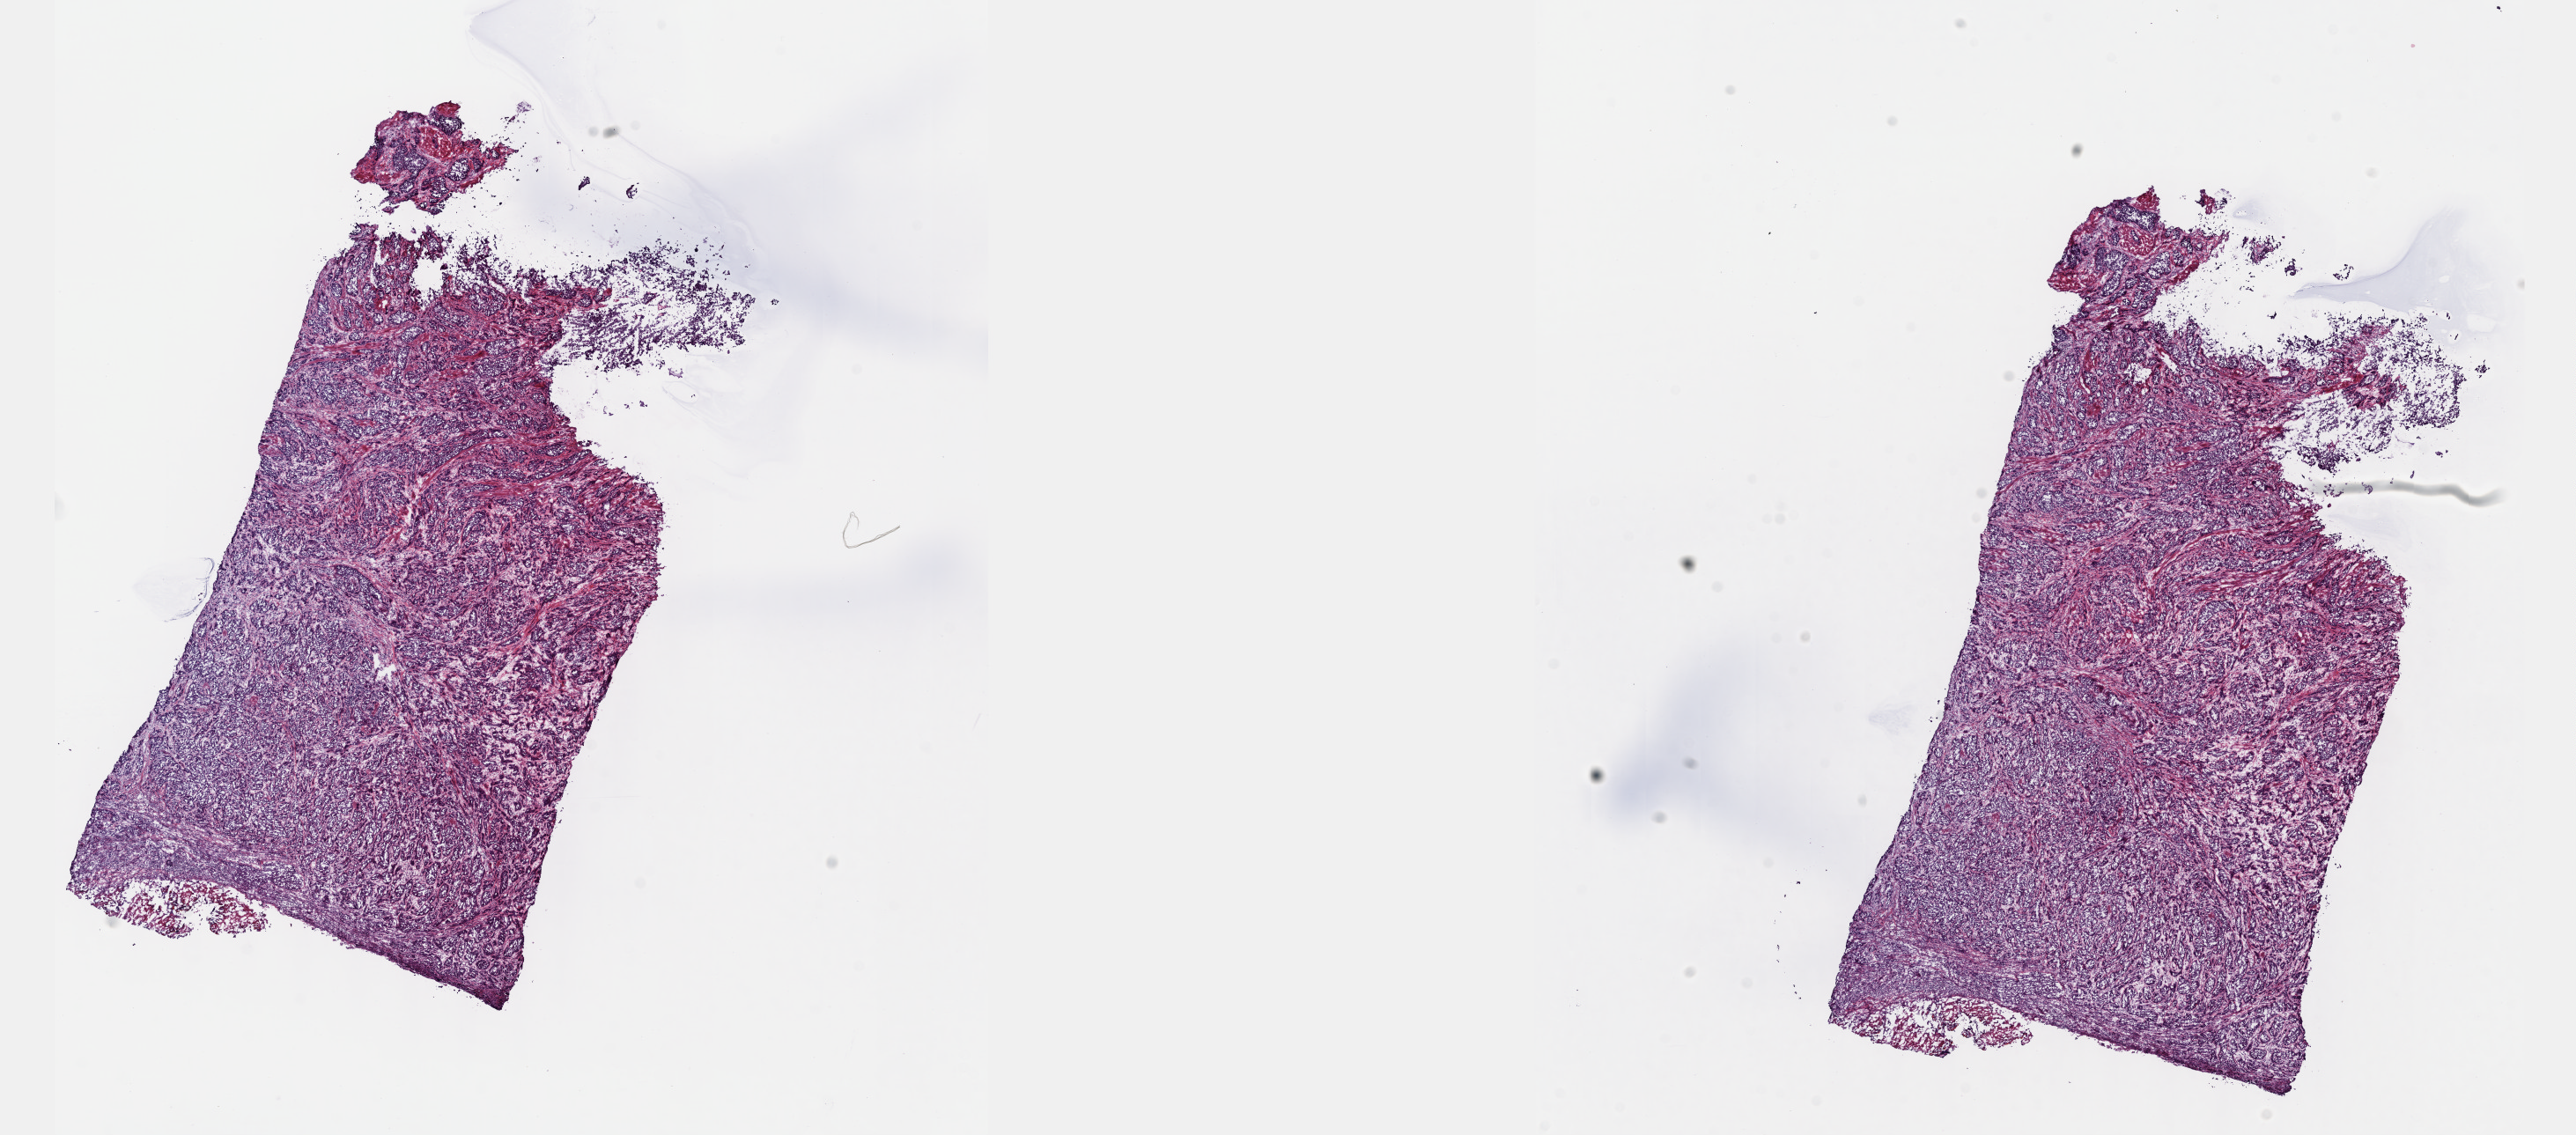
Whole-slide histology image, Hematoxylin and eosin (H&E) stained, whole scanned area (about 23.6 x 10.4 mm, acquisition: 40x scan) shown as a low-resolution overview; frozen section from the top of the tissue portion; bladder, primary tumour sample. Female, age 65 years at initial diagnosis. Histologic grade: high grade. Composition of this section per pathologist review: tumour cells 85%, tumour nuclei 85%, normal cells 0%, stromal cells 15%, necrosis 0%. Infiltration values recorded for this section: lymphocyte infiltration 2%, monocyte infiltration 1%, neutrophil infiltration 4%.
AJCC pathologic stage: II (6th edition). Histologic diagnosis: Transitional cell carcinoma. Lymph nodes positive (case pathology): 0 of 62 examined.